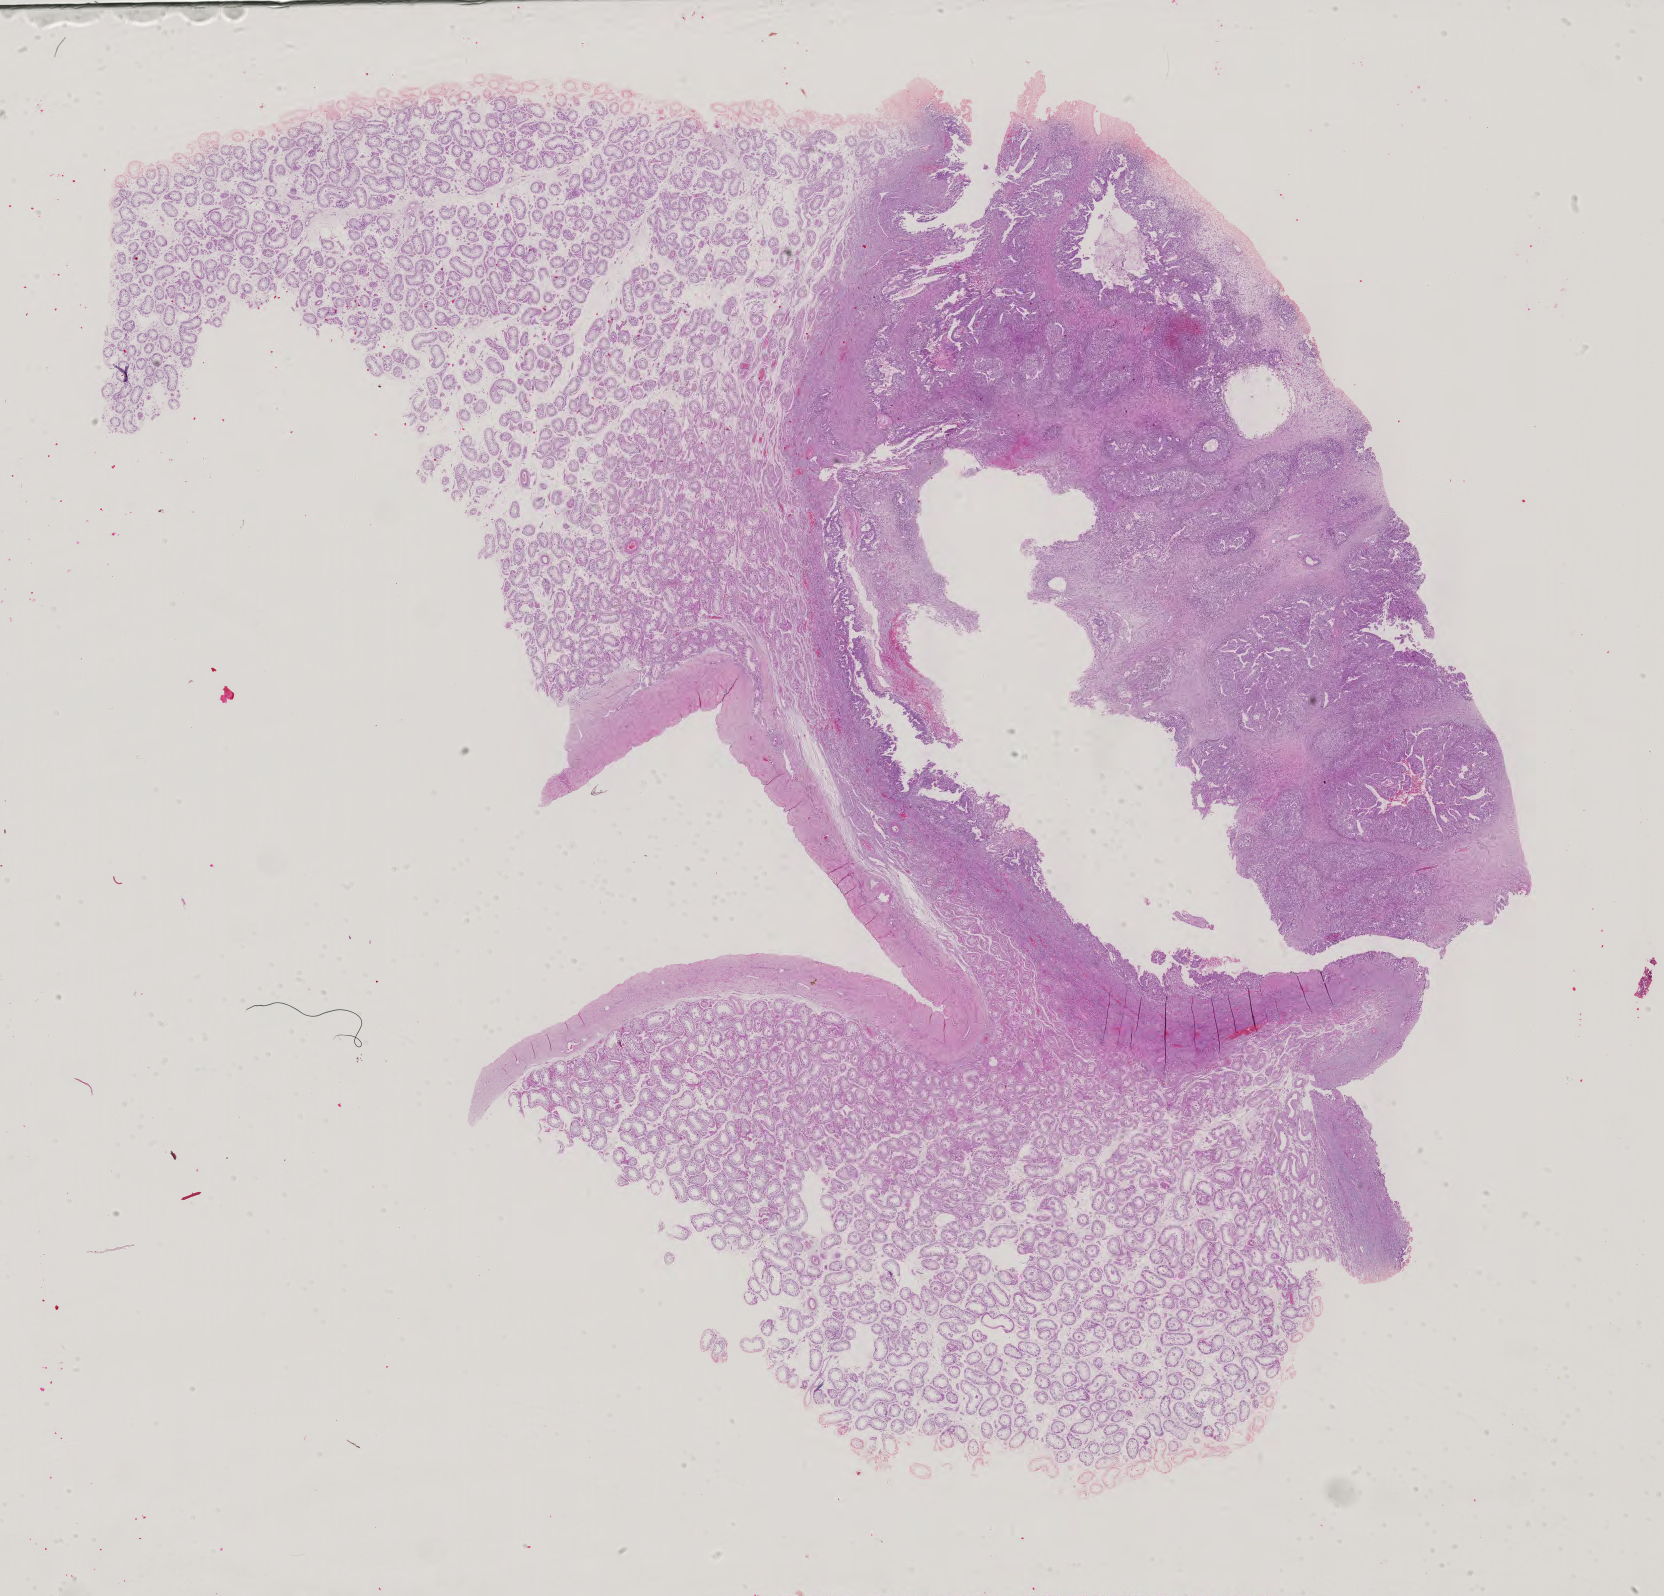
Whole-slide histology image, H&E-stained — shown as a low-resolution overview of the whole scanned area (about 24.2 x 23.3 mm). Male patient.
* specimen: formalin-fixed paraffin-embedded (FFPE) diagnostic section; sample: primary tumour, testis